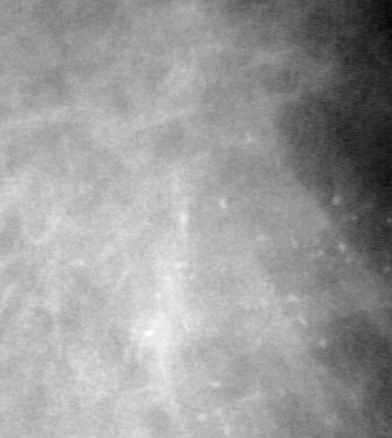
Region of interest cut from a scanned film mammogram (one marked finding), right breast, MLO view, BI-RADS breast density category 3 (scale 1–4).
Finding: mass, shape irregular, margins spiculated; BI-RADS assessment category 5; subtlety rating 4 on a 1 (subtle) to 5 (obvious) scale; pathology (as recorded): malignant.